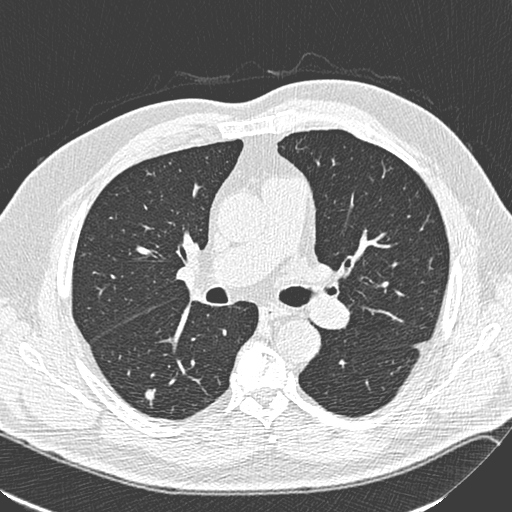
Low-dose screening chest CT, one axial slice; slice 153 of 248 in the series (ordered by position); 120 kVp; lung window (W 1500 / L -600 HU); 512 × 512 image matrix, field of view 357 × 357 mm.
Outlined on this slice (expert manual segmentation):
- lesion 1 (tumor, lower lobe of right lung): box from (x=145, y=389) to (x=155, y=400) px